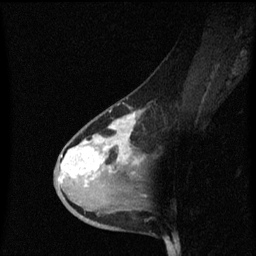
Breast MRI (dynamic contrast-enhanced), one sagittal slice; slice 35 of 60 in the series (ordered by position); dynamic contrast-enhanced series, image 2 of 3 at this slice position (ordered by acquisition); 1.5 T; TE 4.2 ms, TR 8.4 ms; 256 × 256 image matrix, field of view 200 × 200 mm. Female patient, age 38 years. Case-level facts recorded for this patient, not image findings: setting: breast cancer imaged before/during neoadjuvant chemotherapy; receptor status: HR-positive, HER2-negative.
Annotated regions visible in this slice (semi-automatic segmentation, software-assisted and operator-edited):
- analysis volume of interest (the breast-tissue region the enhancement analysis was run in; not a lesion): box from (x=54, y=100) to (x=147, y=205) px
- tumour enhancement mask (voxels above the 70 % enhancement threshold inside the analysis volume of interest): (x=60, y=114)–(x=139, y=183)